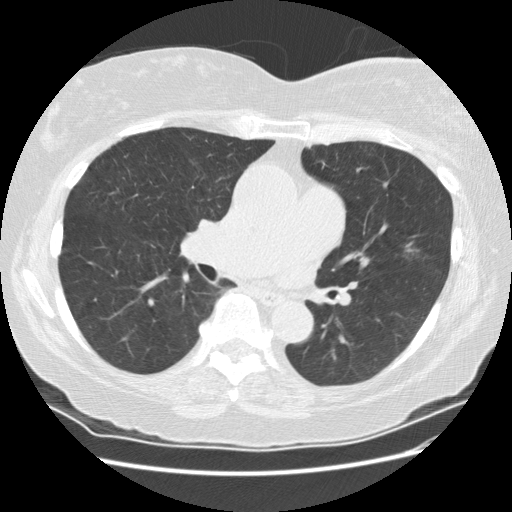
Low-dose screening chest CT, one axial slice. Position 100 of 180 along the scan axis. Reconstruction kernel STANDARD. 120 kVp. Lung window (W 1500 / L -600 HU). 512 × 512 image matrix.
Structures marked on this image (expert manual segmentation):
- lesion 1 (tumor, upper lobe of left lung): box from (x=403, y=247) to (x=420, y=259) px